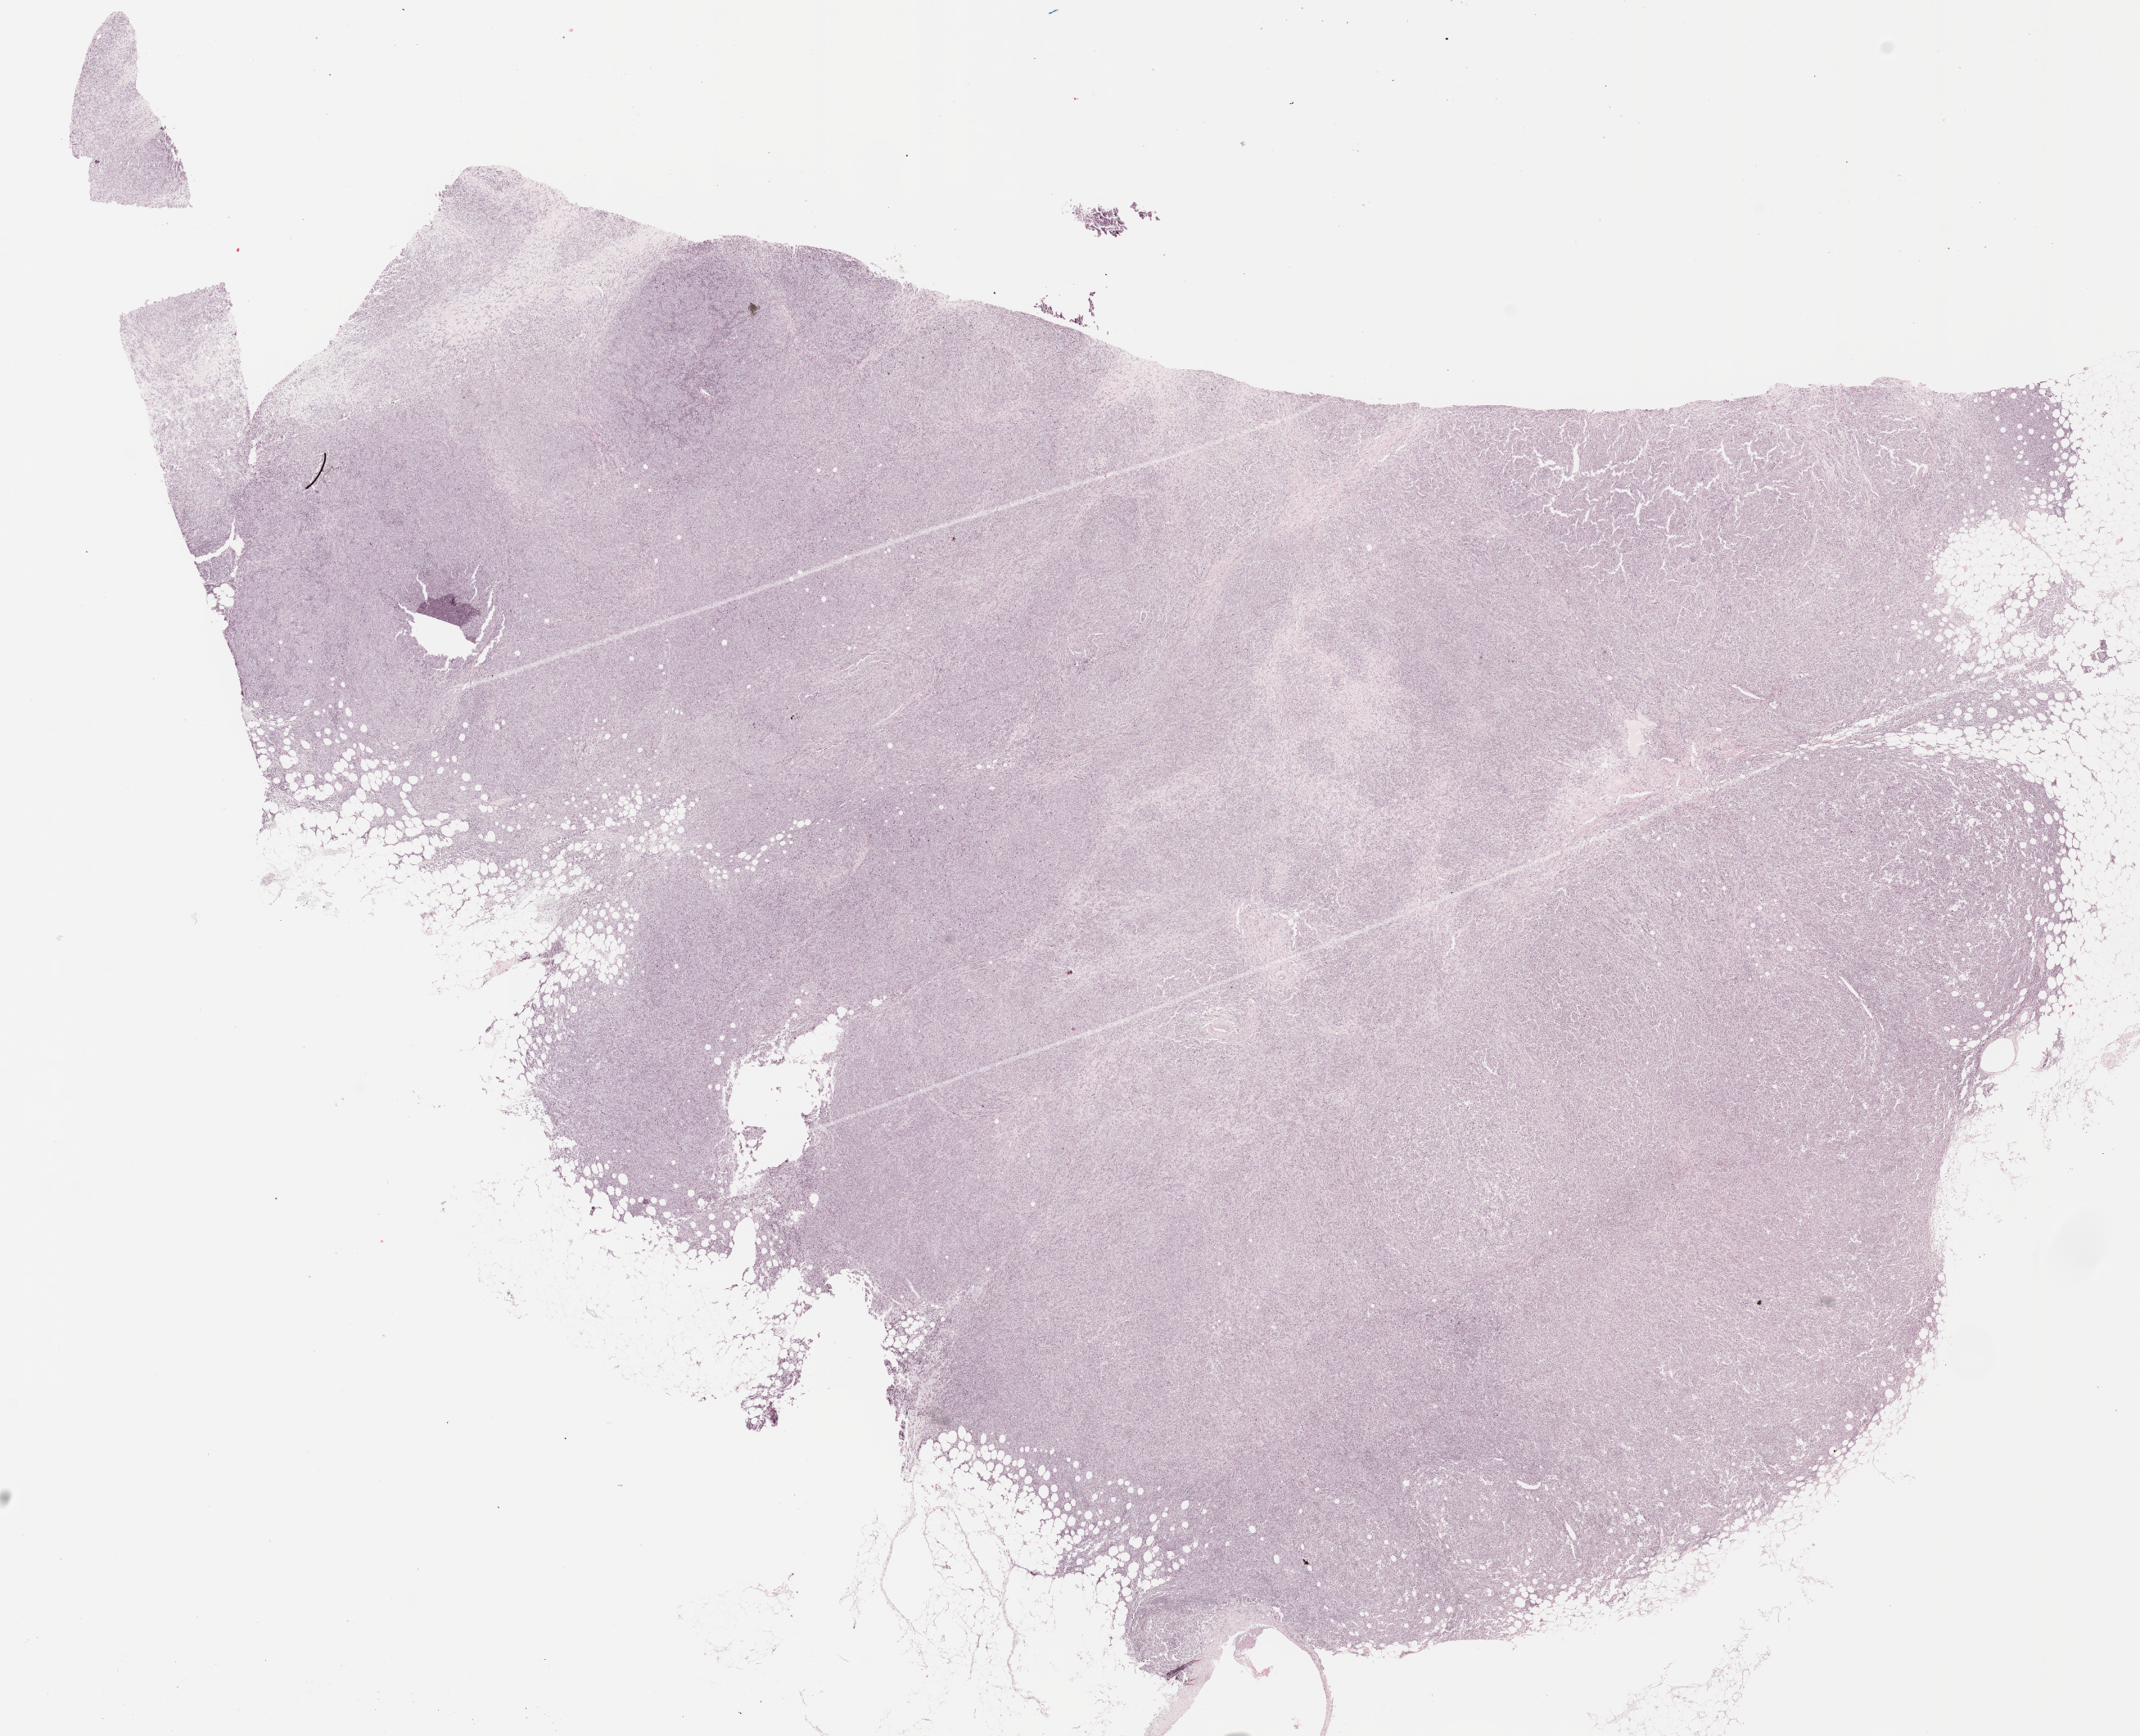
H&E-stained whole-slide image, a low-resolution overview of the entire scanned area, about 20.9 x 16.9 mm (acquisition: 20x scan); FFPE section; sample: primary tumour, breast. Female patient; age at initial diagnosis 61 years.
Diagnosis: Infiltrating duct carcinoma, NOS. AJCC pathologic stage: IIA. Laterality: right. TNM: T2 N0 (i-) M0. Lymph nodes positive (case pathology): 0 of 15 examined.